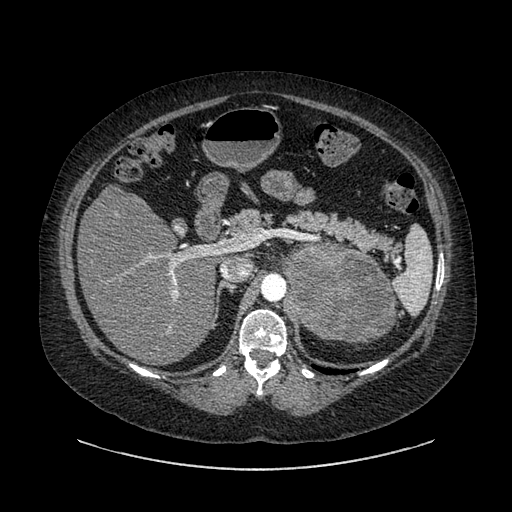
Contrast-enhanced abdominal CT, one axial slice. Position 575 of 769 along the scan axis. Intravenous contrast given. Soft-tissue window (W 400 / L 40 HU). 0.62 mm slice thickness. 512 × 512 image matrix, field of view 460 × 460 mm. Patient: female, 61 years. From the clinical record (not read from this slice): diagnosis: adrenocortical carcinoma; tumour side: left adrenal.
Outlined on this slice (semi-automatically segmented with operator editing):
- mass: bounding box (x1, y1, x2, y2) in pixels: (282, 243, 394, 342)